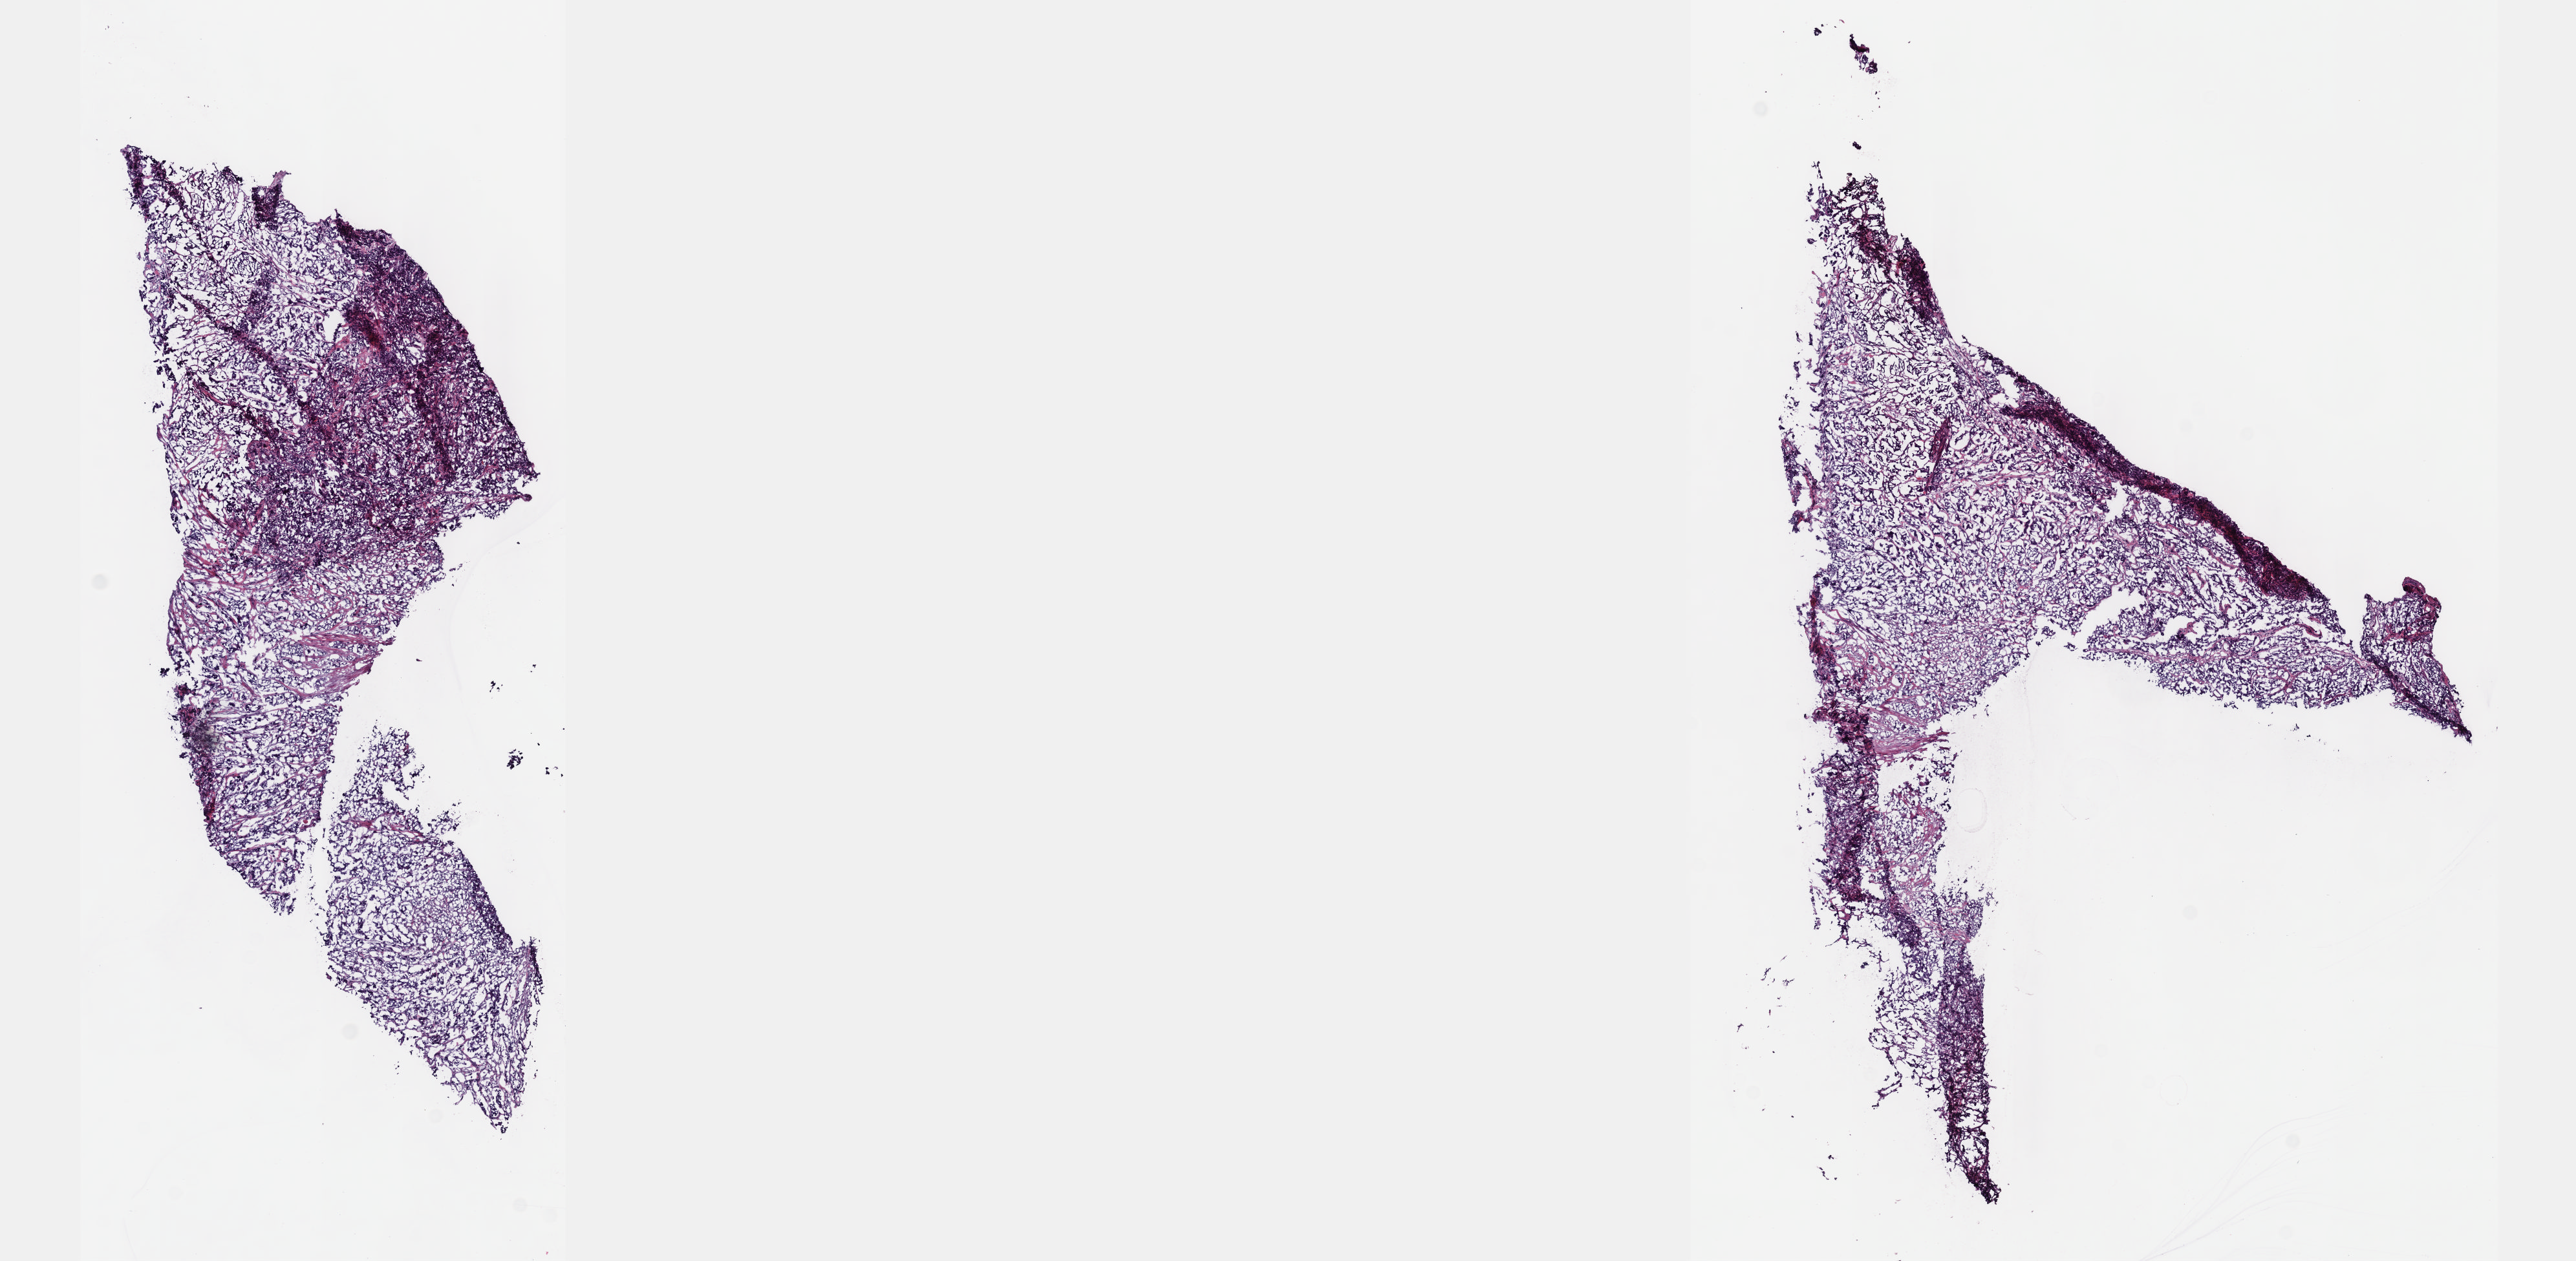
H&E-stained whole-slide image — shown as a low-resolution overview of the whole scanned area (about 16.1 x 7.9 mm, from a 40x scan); frozen section from the top of the tissue portion; sample: primary tumour, bladder. Male patient; age at initial diagnosis 74 years. Histologic grade: high grade. Slide review estimates, as recorded: tumour cells 80%, tumour nuclei 80%, normal cells 0%, stromal cells 20%, necrosis 0%. Inflammatory infiltration, as recorded: lymphocyte infiltration 3%, monocyte infiltration 2%, neutrophil infiltration 5%.
* AJCC pathologic stage: IV
* histologic diagnosis: Transitional cell carcinoma (lateral wall of bladder)